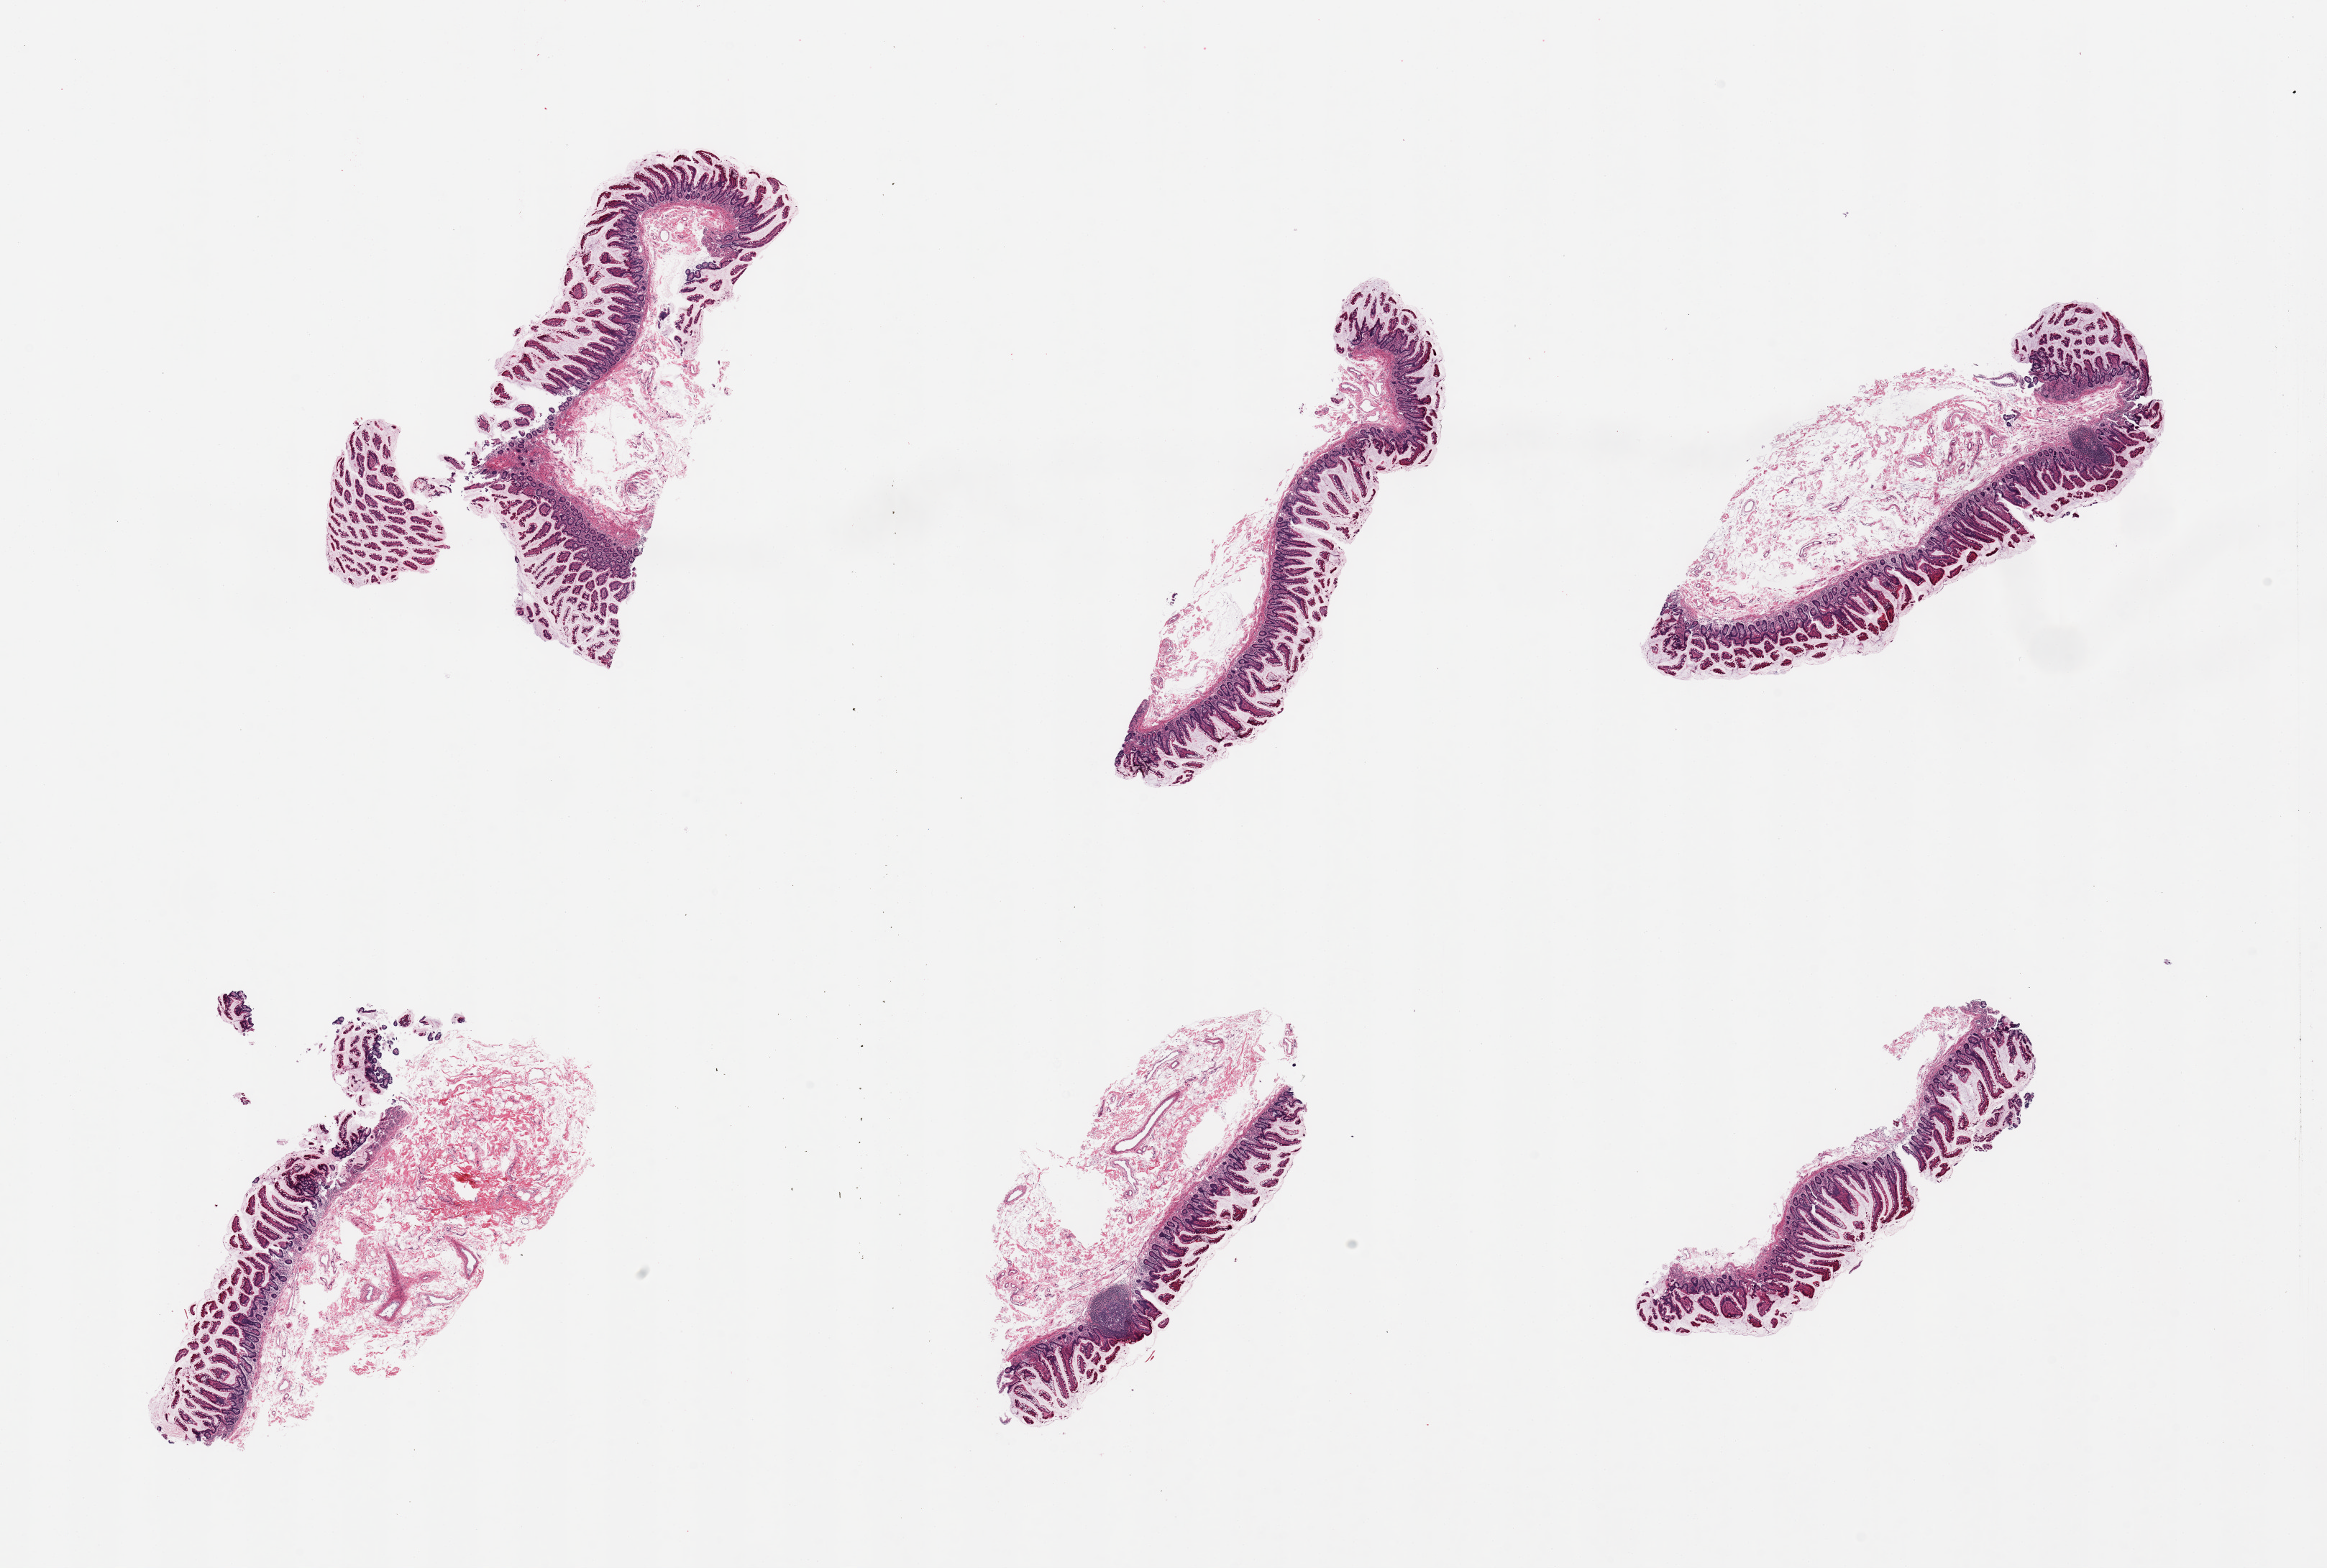
Hematoxylin and eosin (H&E) whole-slide image — whole scanned area (about 25.6 x 17.3 mm, acquisition: 20x scan) shown as a low-resolution overview. Donor: male.
* specimen: PAXgene-fixed, paraffin-embedded tissue; sampled site (target tissue): ileum; tissue donor sample